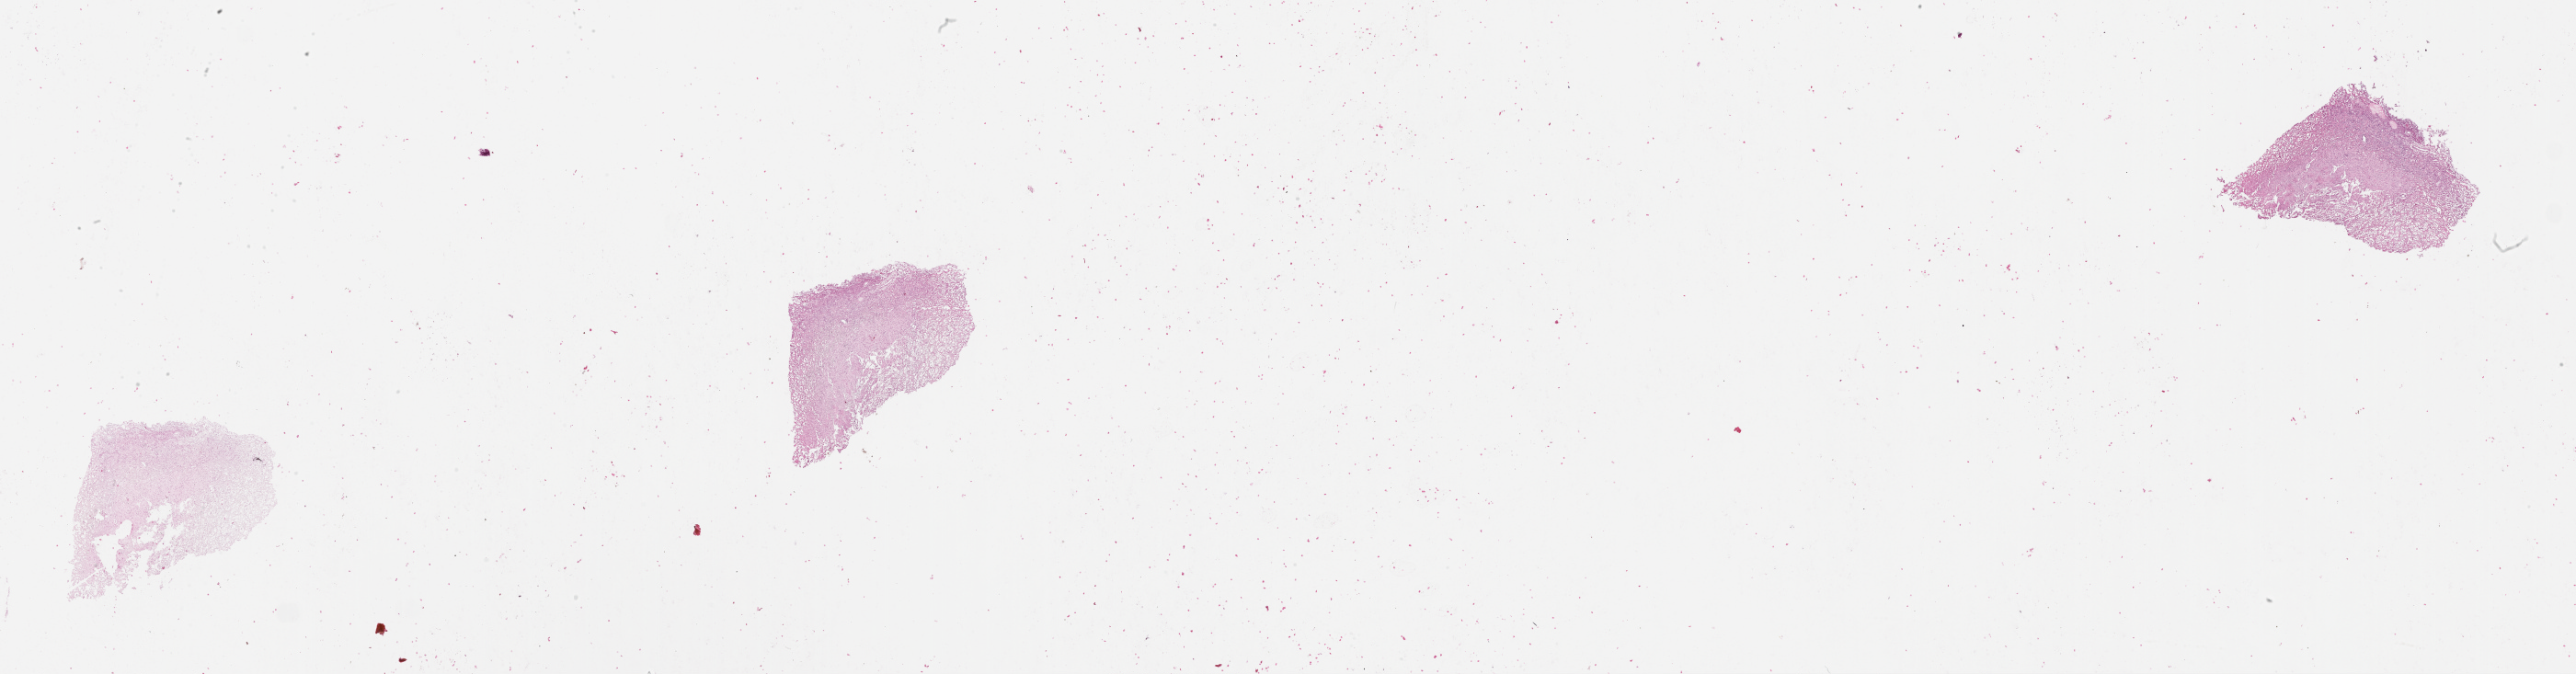
Hematoxylin and eosin (H&E) stained whole-slide image, low-resolution overview of the scanned area, about 45.1 x 11.8 mm (slide scanned at 20x); tumour tissue sample, sampled site: brain. Male, 61 y/o. Composition of this section per pathologist review: tumour nuclei 60%, necrosis 10%.
• diagnosis: Glioblastoma
• primary tumour site (as recorded): parietal lobe